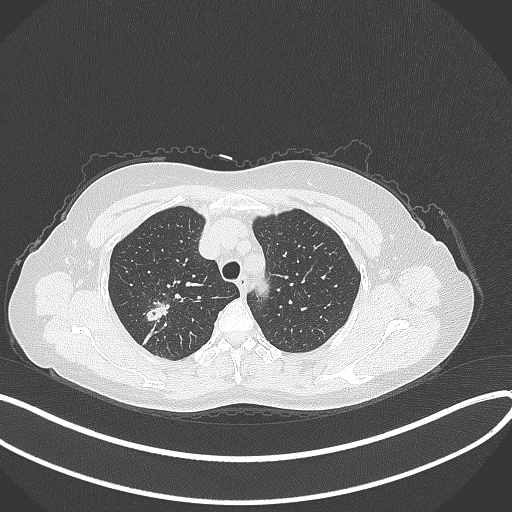
Chest CT, one axial slice. Position 287 of 337 along the scan axis. Reconstruction kernel B70f. 120 kVp. Lung window (W 1500 / L -600 HU). 1 mm slice thickness. 512 × 512 image matrix, field of view 400 × 400 mm. Patient: female, 50 years. From the clinical record (not read from this slice): clinical TNM (as recorded): T1c N0 M0; histopathological grade: G2-3.
Outlined on this slice (rectangle marked by the reading radiologist):
- lung tumour (recorded histology: adenocarcinoma): bounding box <141,297,173,327> (left, top, right, bottom; pixels)